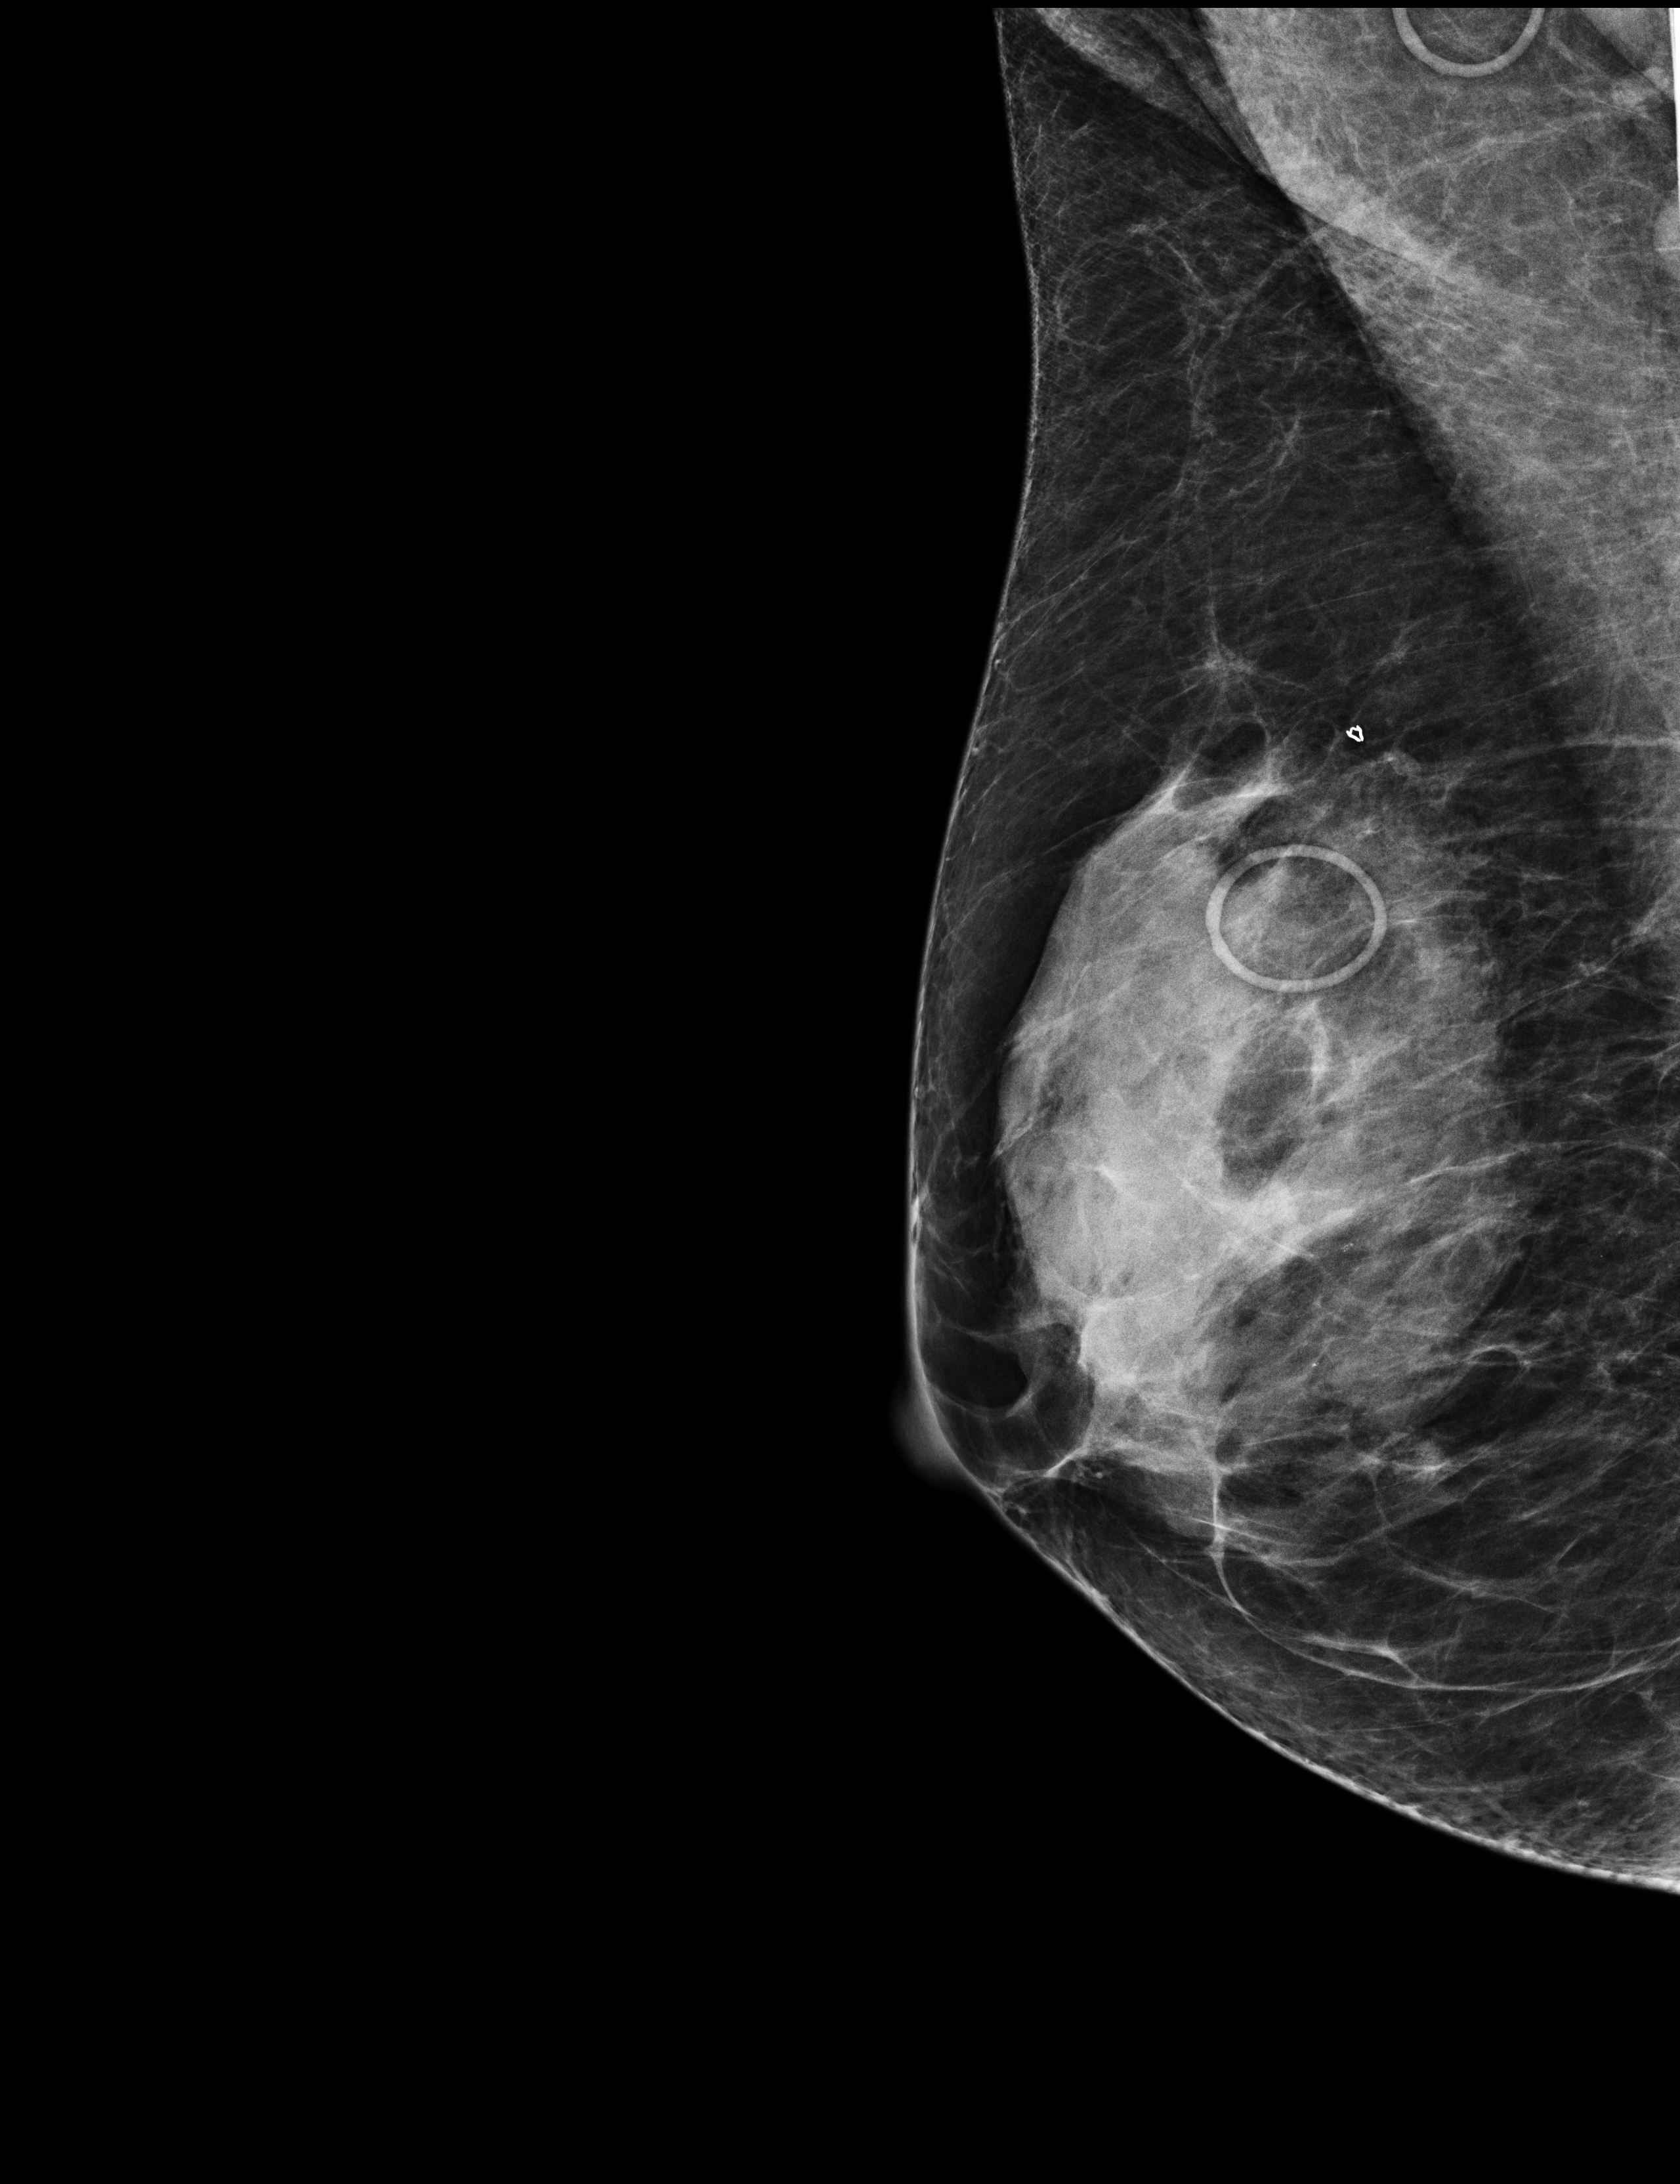
Screening examination. Patient: female, 66 years.
Image type: full-field digital mammogram. Breast: right. Projection: MLO view. BI-RADS breast density category at the screening exam (both breasts, scale 1–4): 3. Final BI-RADS assessment for this screening round (tomosynthesis exam, both breasts): category 1. Recall: no recall after this screen.